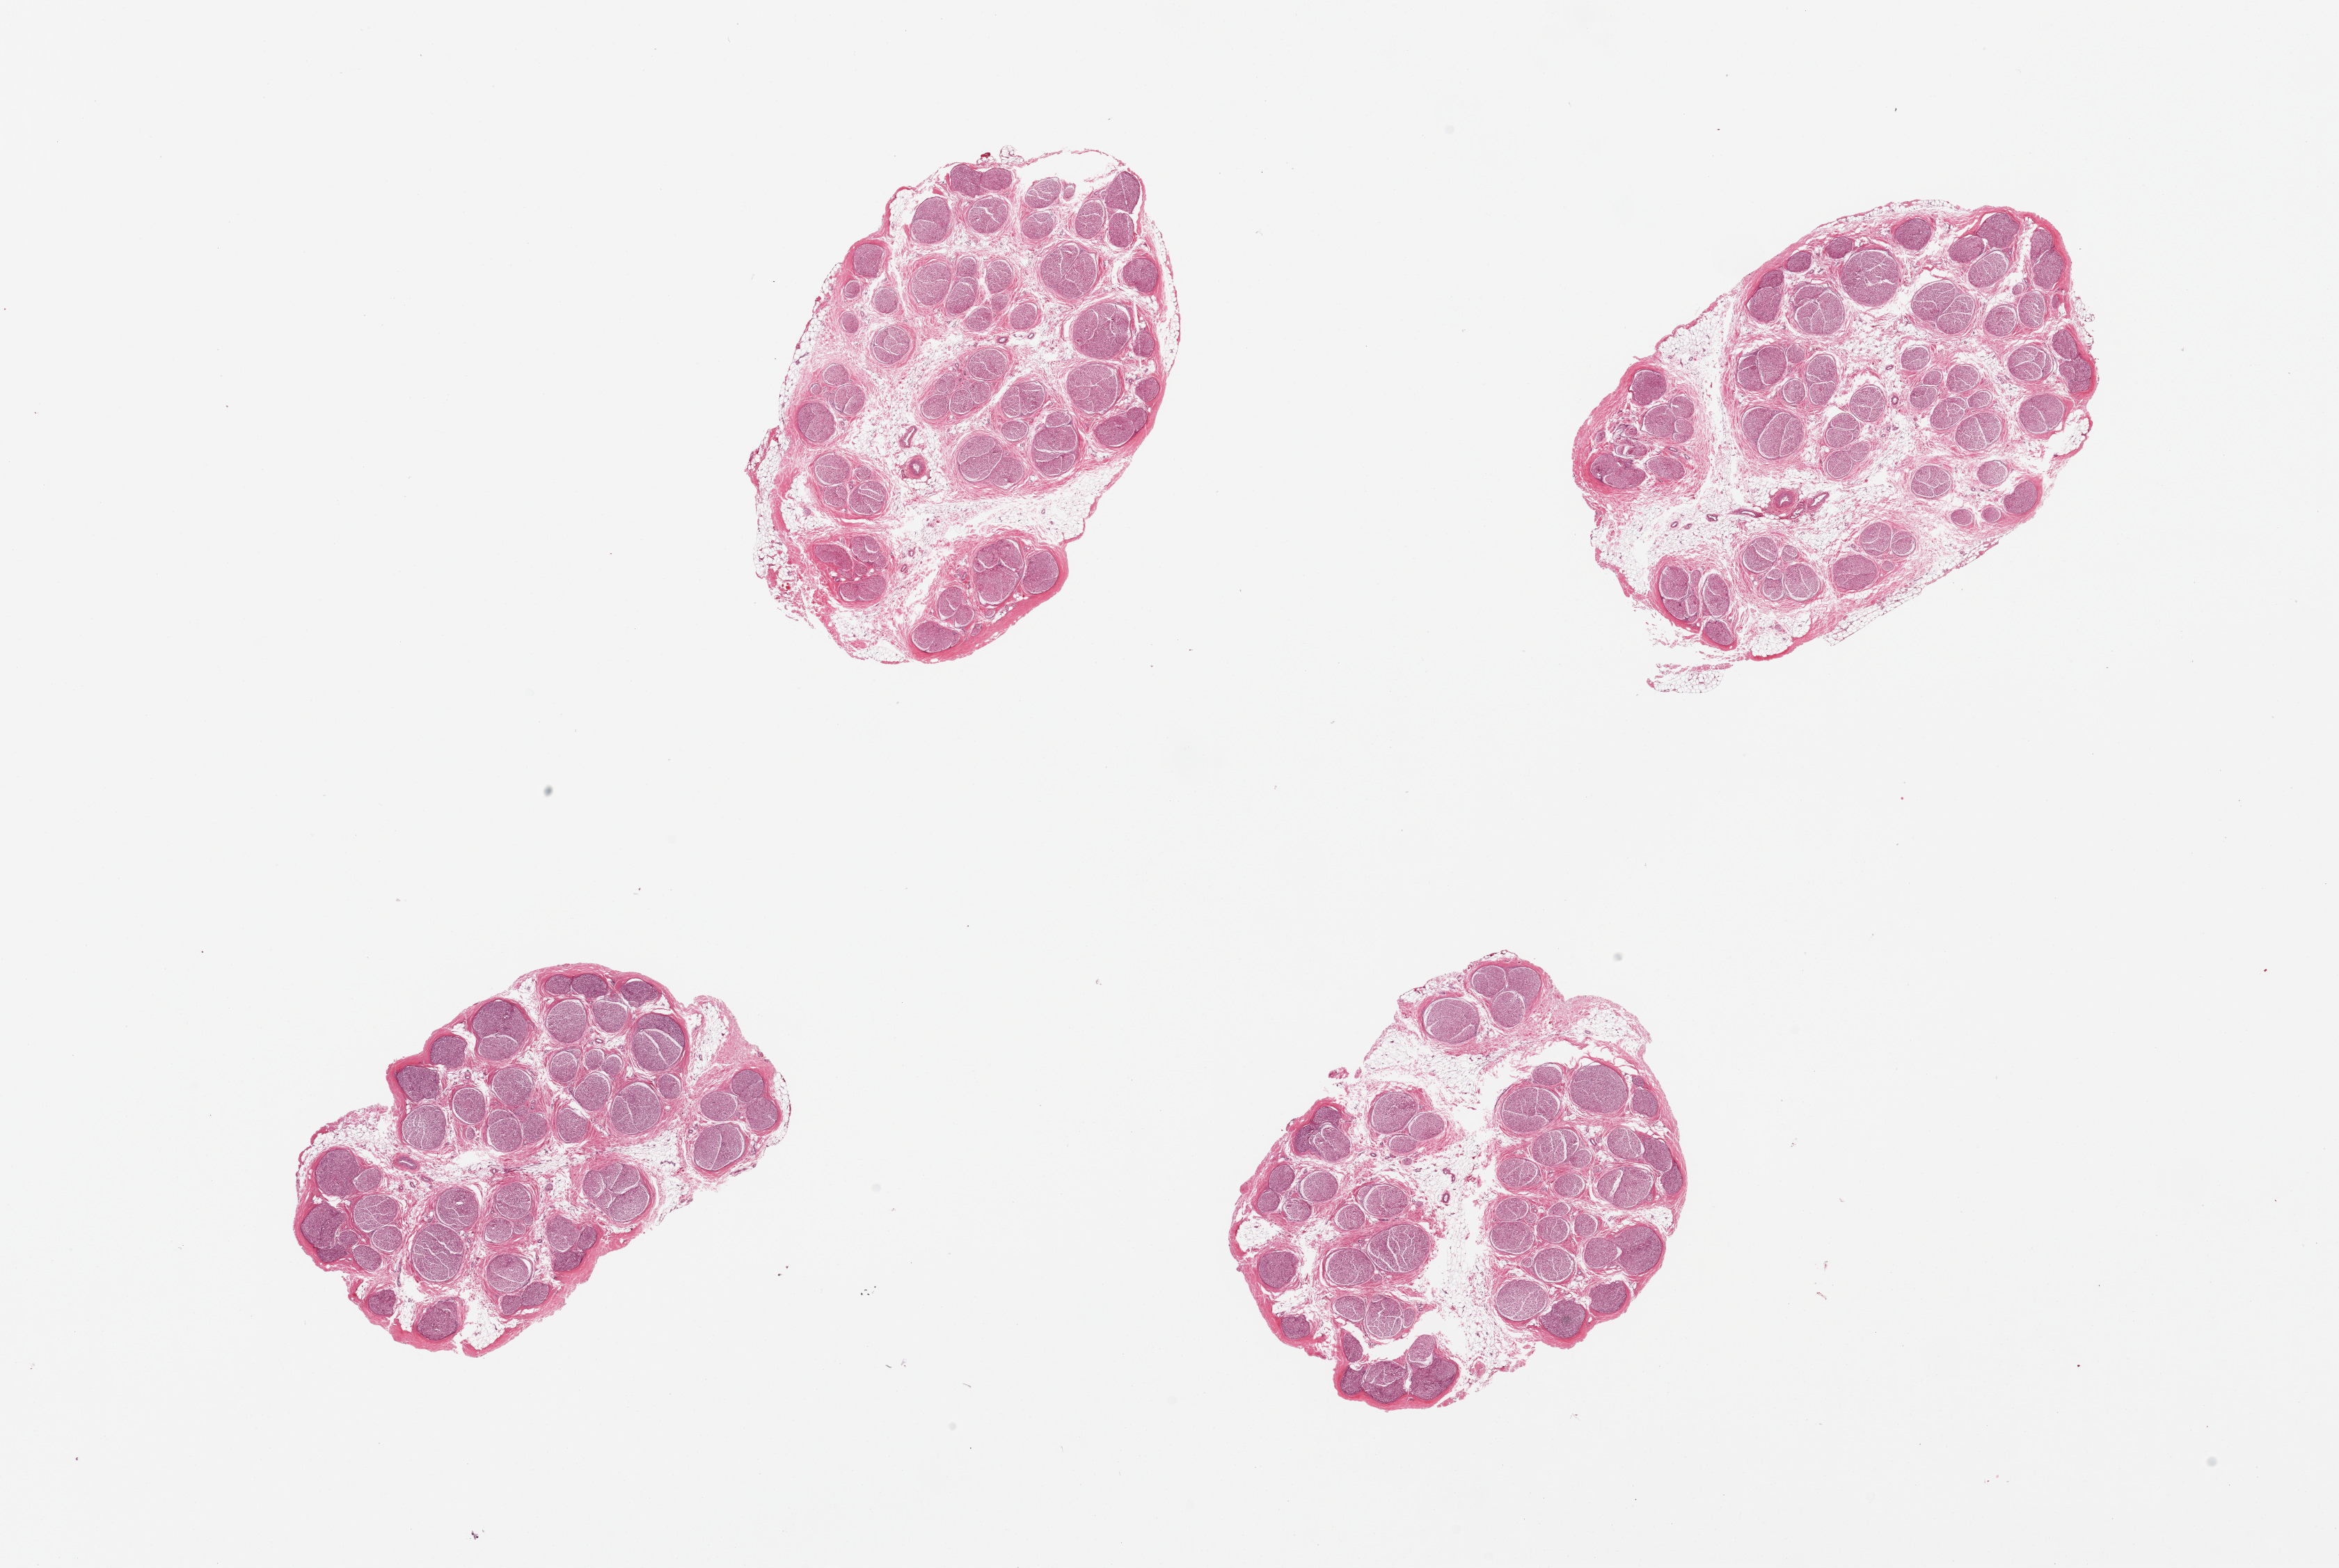
Digitized H&E-stained section — a low-resolution overview of the entire scanned area, about 26.6 x 17.8 mm (acquisition: 20x scan), PAXgene-fixed paraffin-embedded (PFPE) section, sampled site (target tissue): tibial nerve, donor tissue sample. Donor sex: female.
Reviewer comment on this tissue sample: 4 pieces, good clean specimens.